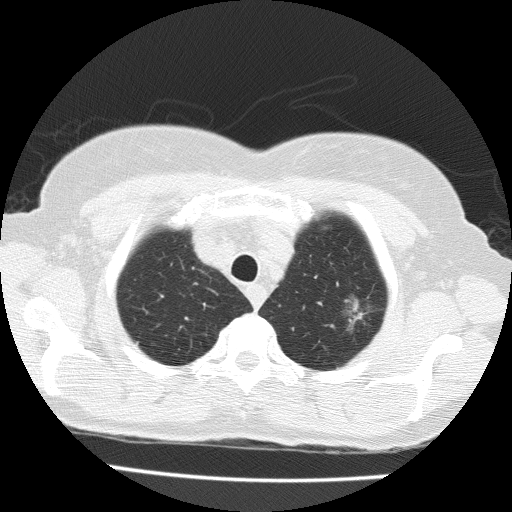
Axial slice from a low-dose chest CT screening exam; baseline annual screen; lung window (W 1500 / L -600 HU); 2 mm slice thickness; slice 27 of 183 in the series. Female participant, aged 71 years at enrolment. Former smoker at enrolment.
Lesion marked by an expert reader, bounding box <337,291,390,338> (left, top, right, bottom; pixels). Screening reader's record for this exam (one nodule recorded; not confirmed to be the boxed lesion): non-calcified nodule or mass ≥4 mm, left upper lobe, 15 × 10 mm, spiculated (stellate) margins, soft tissue attenuation. Later outcome: lung cancer diagnosed 49 days after this screen — adenocarcinoma with mixed subtypes, left upper lobe, well differentiated (G1), stage IA (AJCC 6th edition), 15 mm at pathology.